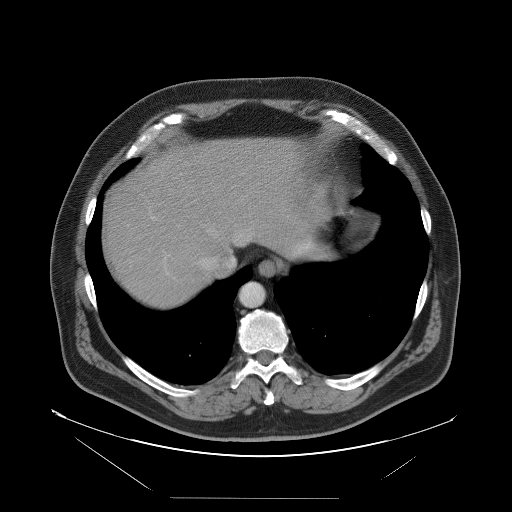
Contrast-enhanced abdominal CT, one axial slice; slice 86 of 114 in the series (ordered by position); intravenous contrast given; soft-tissue window (W 400 / L 40 HU); 512 × 512 image matrix, field of view 500 × 500 mm. Male patient, age 61 years. Case-level facts recorded for this patient, not image findings: diagnosis: colorectal cancer liver metastases, imaged before liver resection; multiple liver metastases: no; largest metastasis: 6.5 cm; disease in both lobes: yes.
Structures marked on this image (expert manual segmentation):
- hepatic veins: box from (x=196, y=225) to (x=251, y=270) px
- liver: (x=104, y=137)–(x=308, y=307)
- planned liver remnant (the part of the liver to remain after resection): (x=156, y=137)–(x=309, y=257)